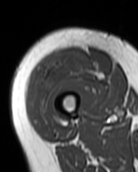
MRI of an extremity soft-tissue mass, one axial slice. Position 27 of 99 along the scan axis. MR volume resampled by the dataset authors to the PET/CT grid (not the native acquisition matrix). 3.27 mm slice thickness. 138 × 172 image matrix, field of view 135 × 168 mm. Female patient. Case-level facts recorded for this patient, not image findings: histological type: pleiomorphic undifferentiated sarcoma; grade: high; site of the primary tumour: right quadricep.
Outlined on this slice (expert contour drawn on MRI and transferred to this co-registered scan by the dataset authors):
- gross tumour volume including surrounding oedema: box from (x=30, y=52) to (x=102, y=126) px